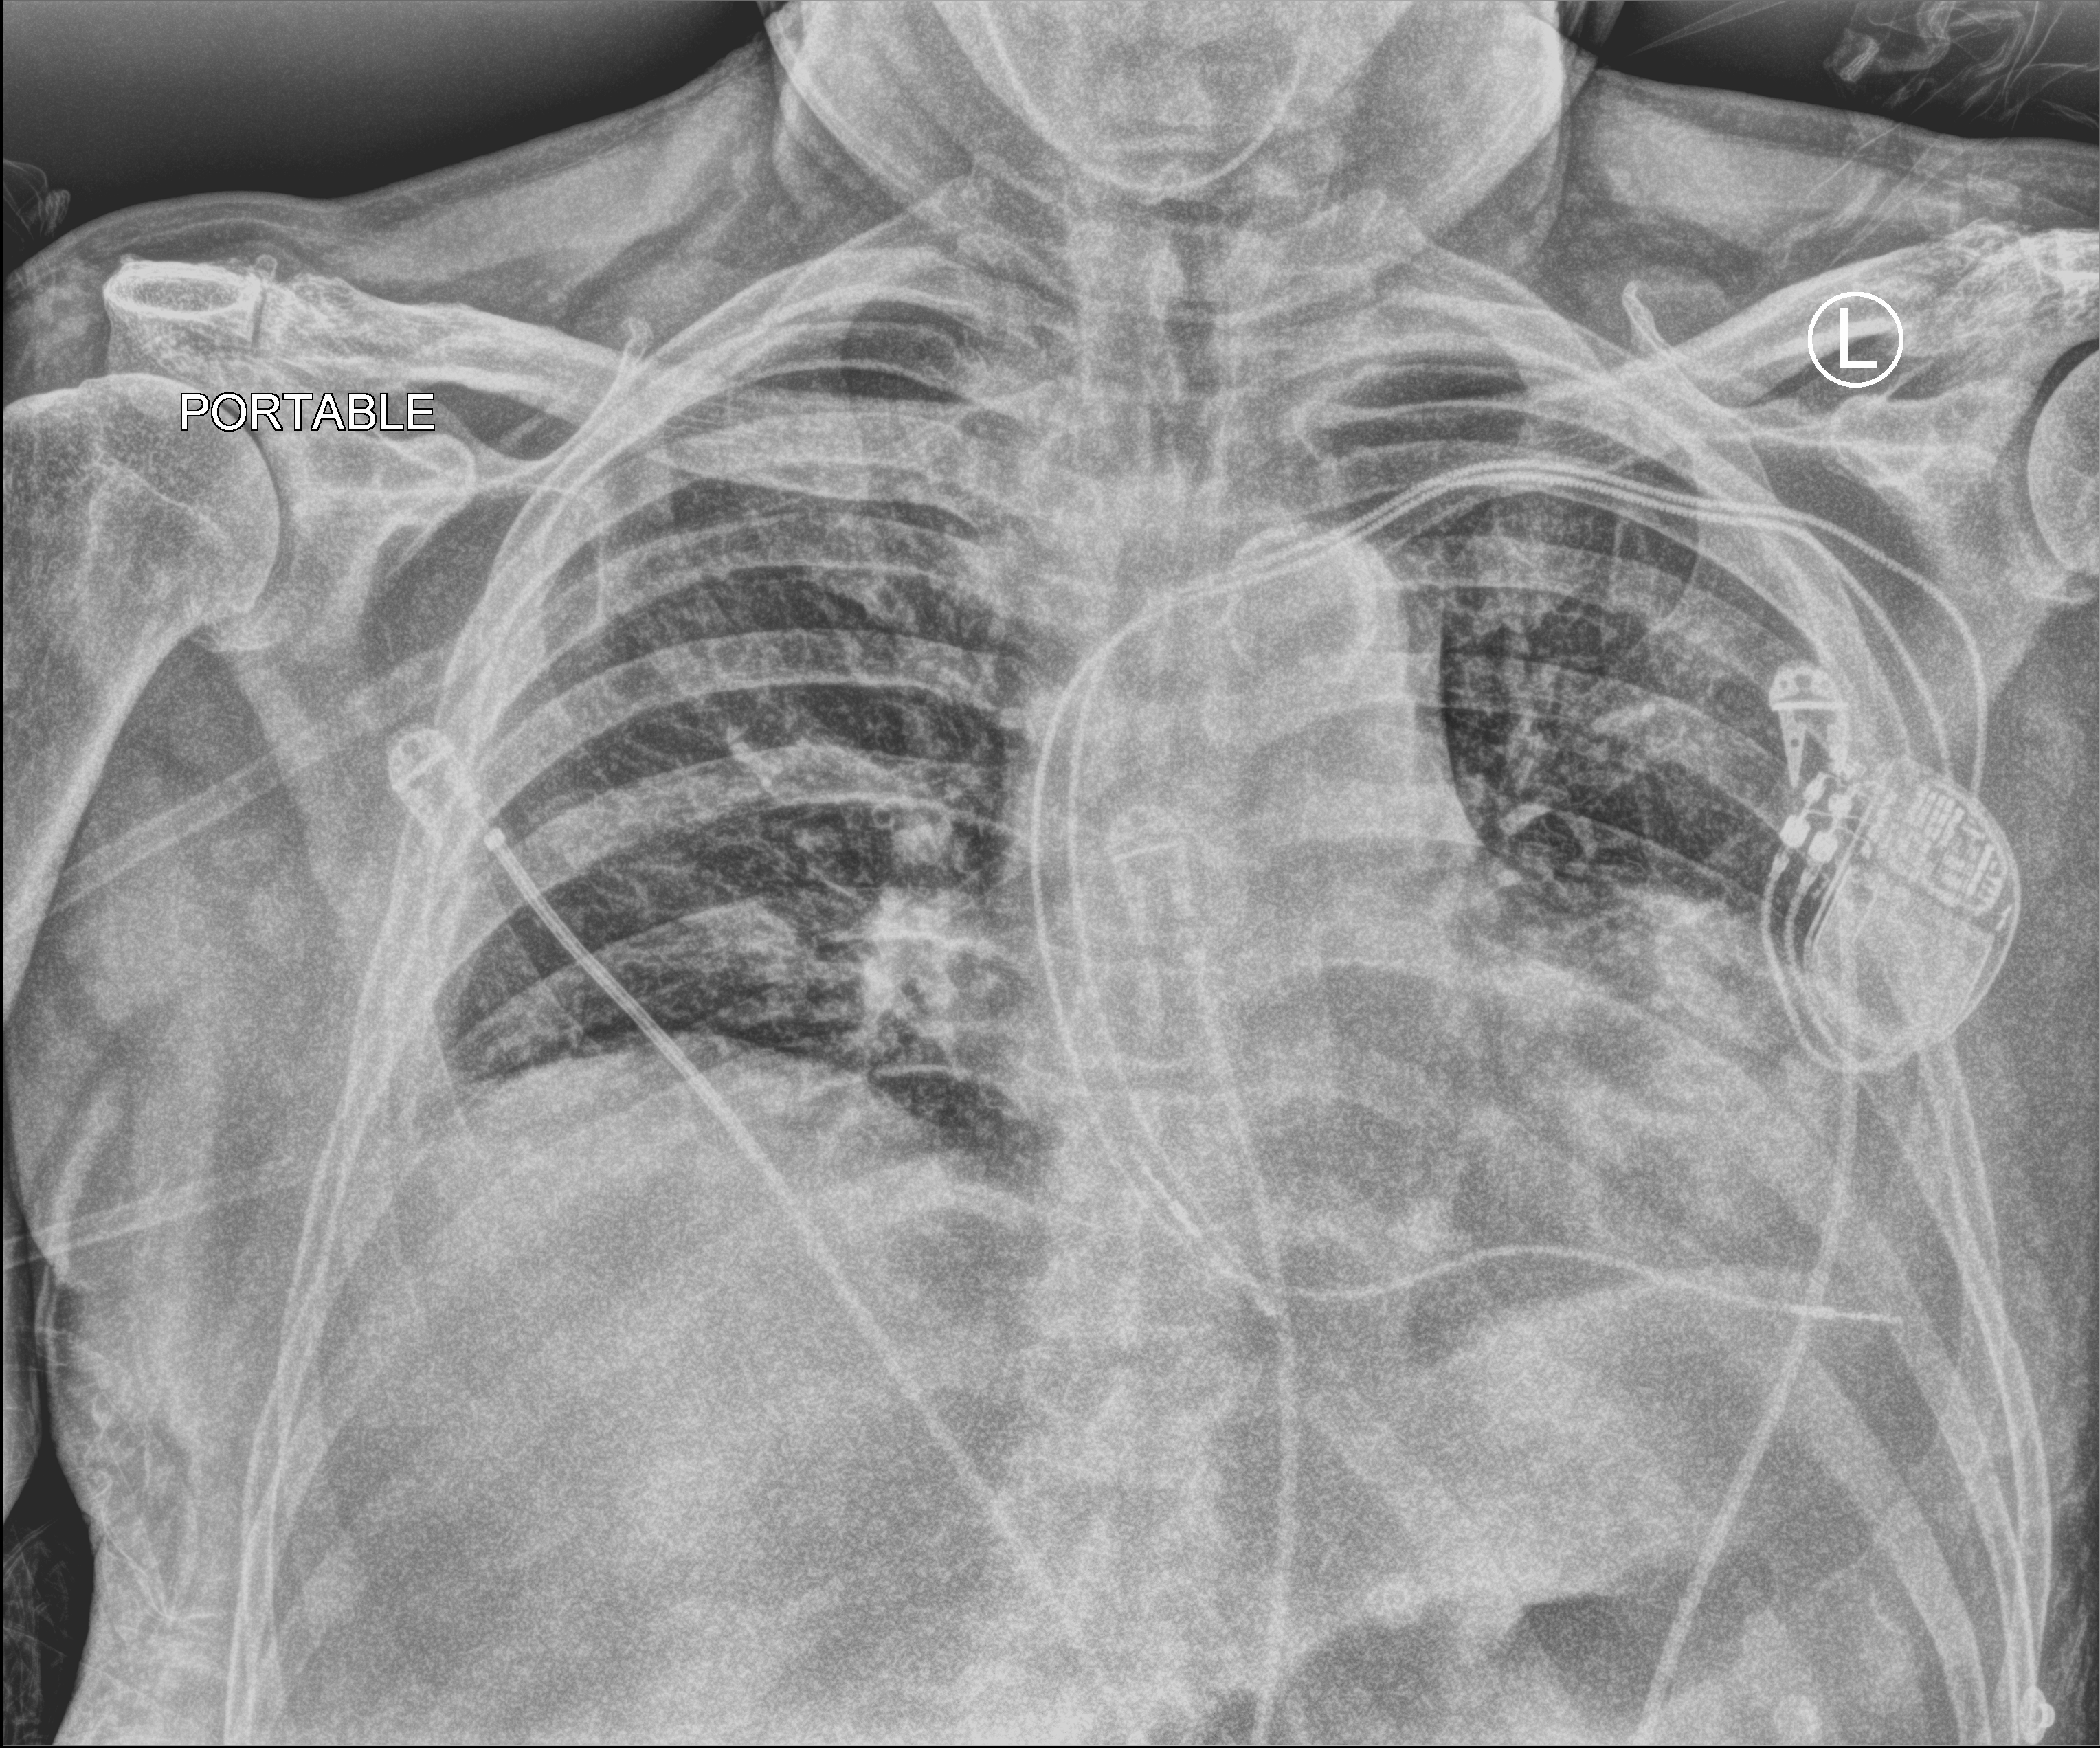
Bedside chest radiograph (computed radiography); anteroposterior (AP) projection. Male patient hospitalised with COVID-19, age 60–74 years.
Hospital-stay facts (about this admission, not read from this image; timing relative to this image not recorded): mechanically ventilated during this hospital stay: yes.